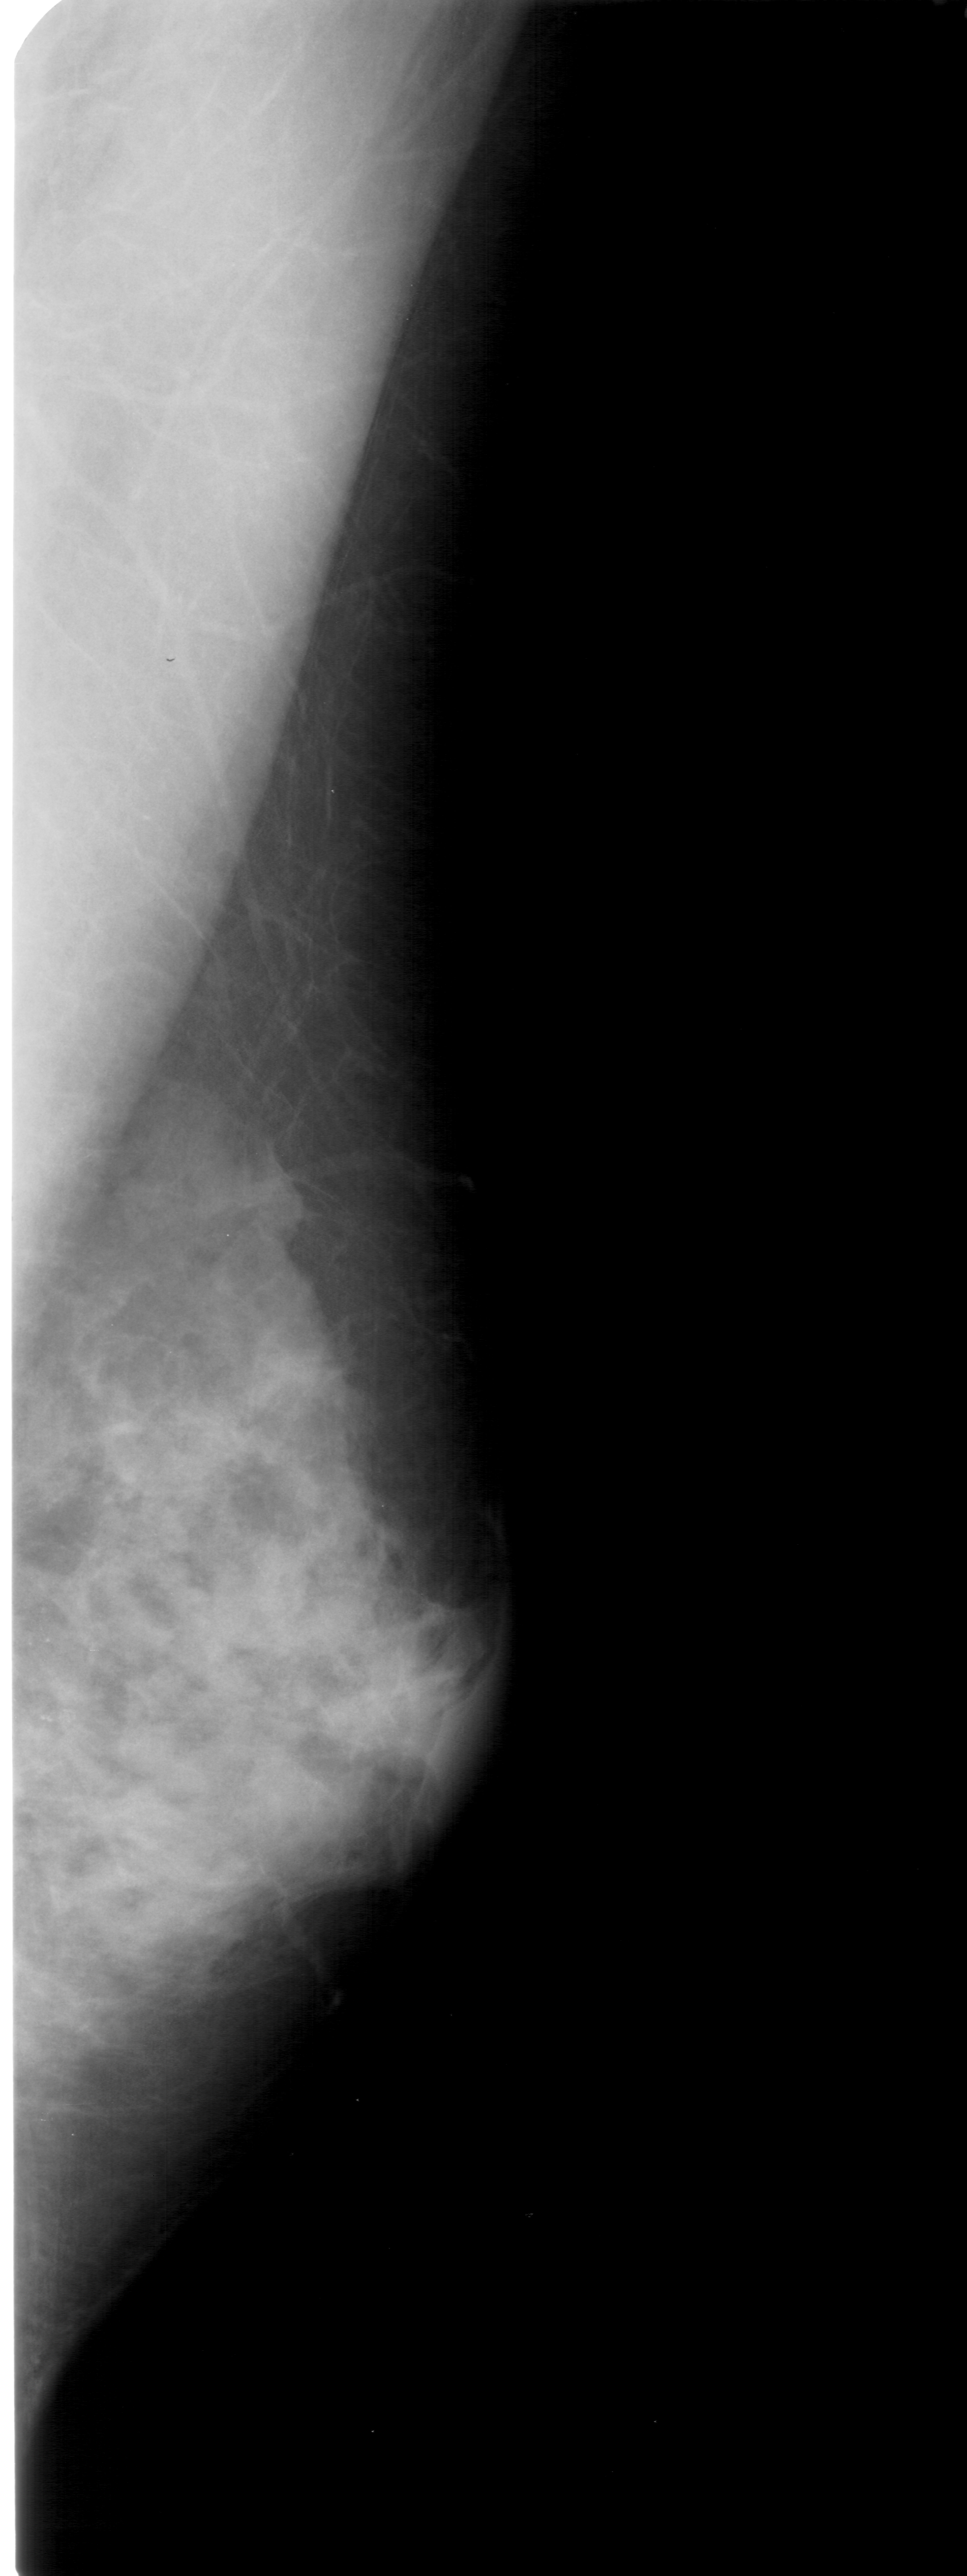
Digitized screen-film mammogram, right breast, mediolateral oblique (MLO) view, BI-RADS breast density category 4 (scale 1–4).
Abnormality record for this image: calcifications, morphology pleomorphic, distribution clustered; BI-RADS assessment category 4; subtlety rating 2 on a 1 (subtle) to 5 (obvious) scale; pathology (as recorded): benign.